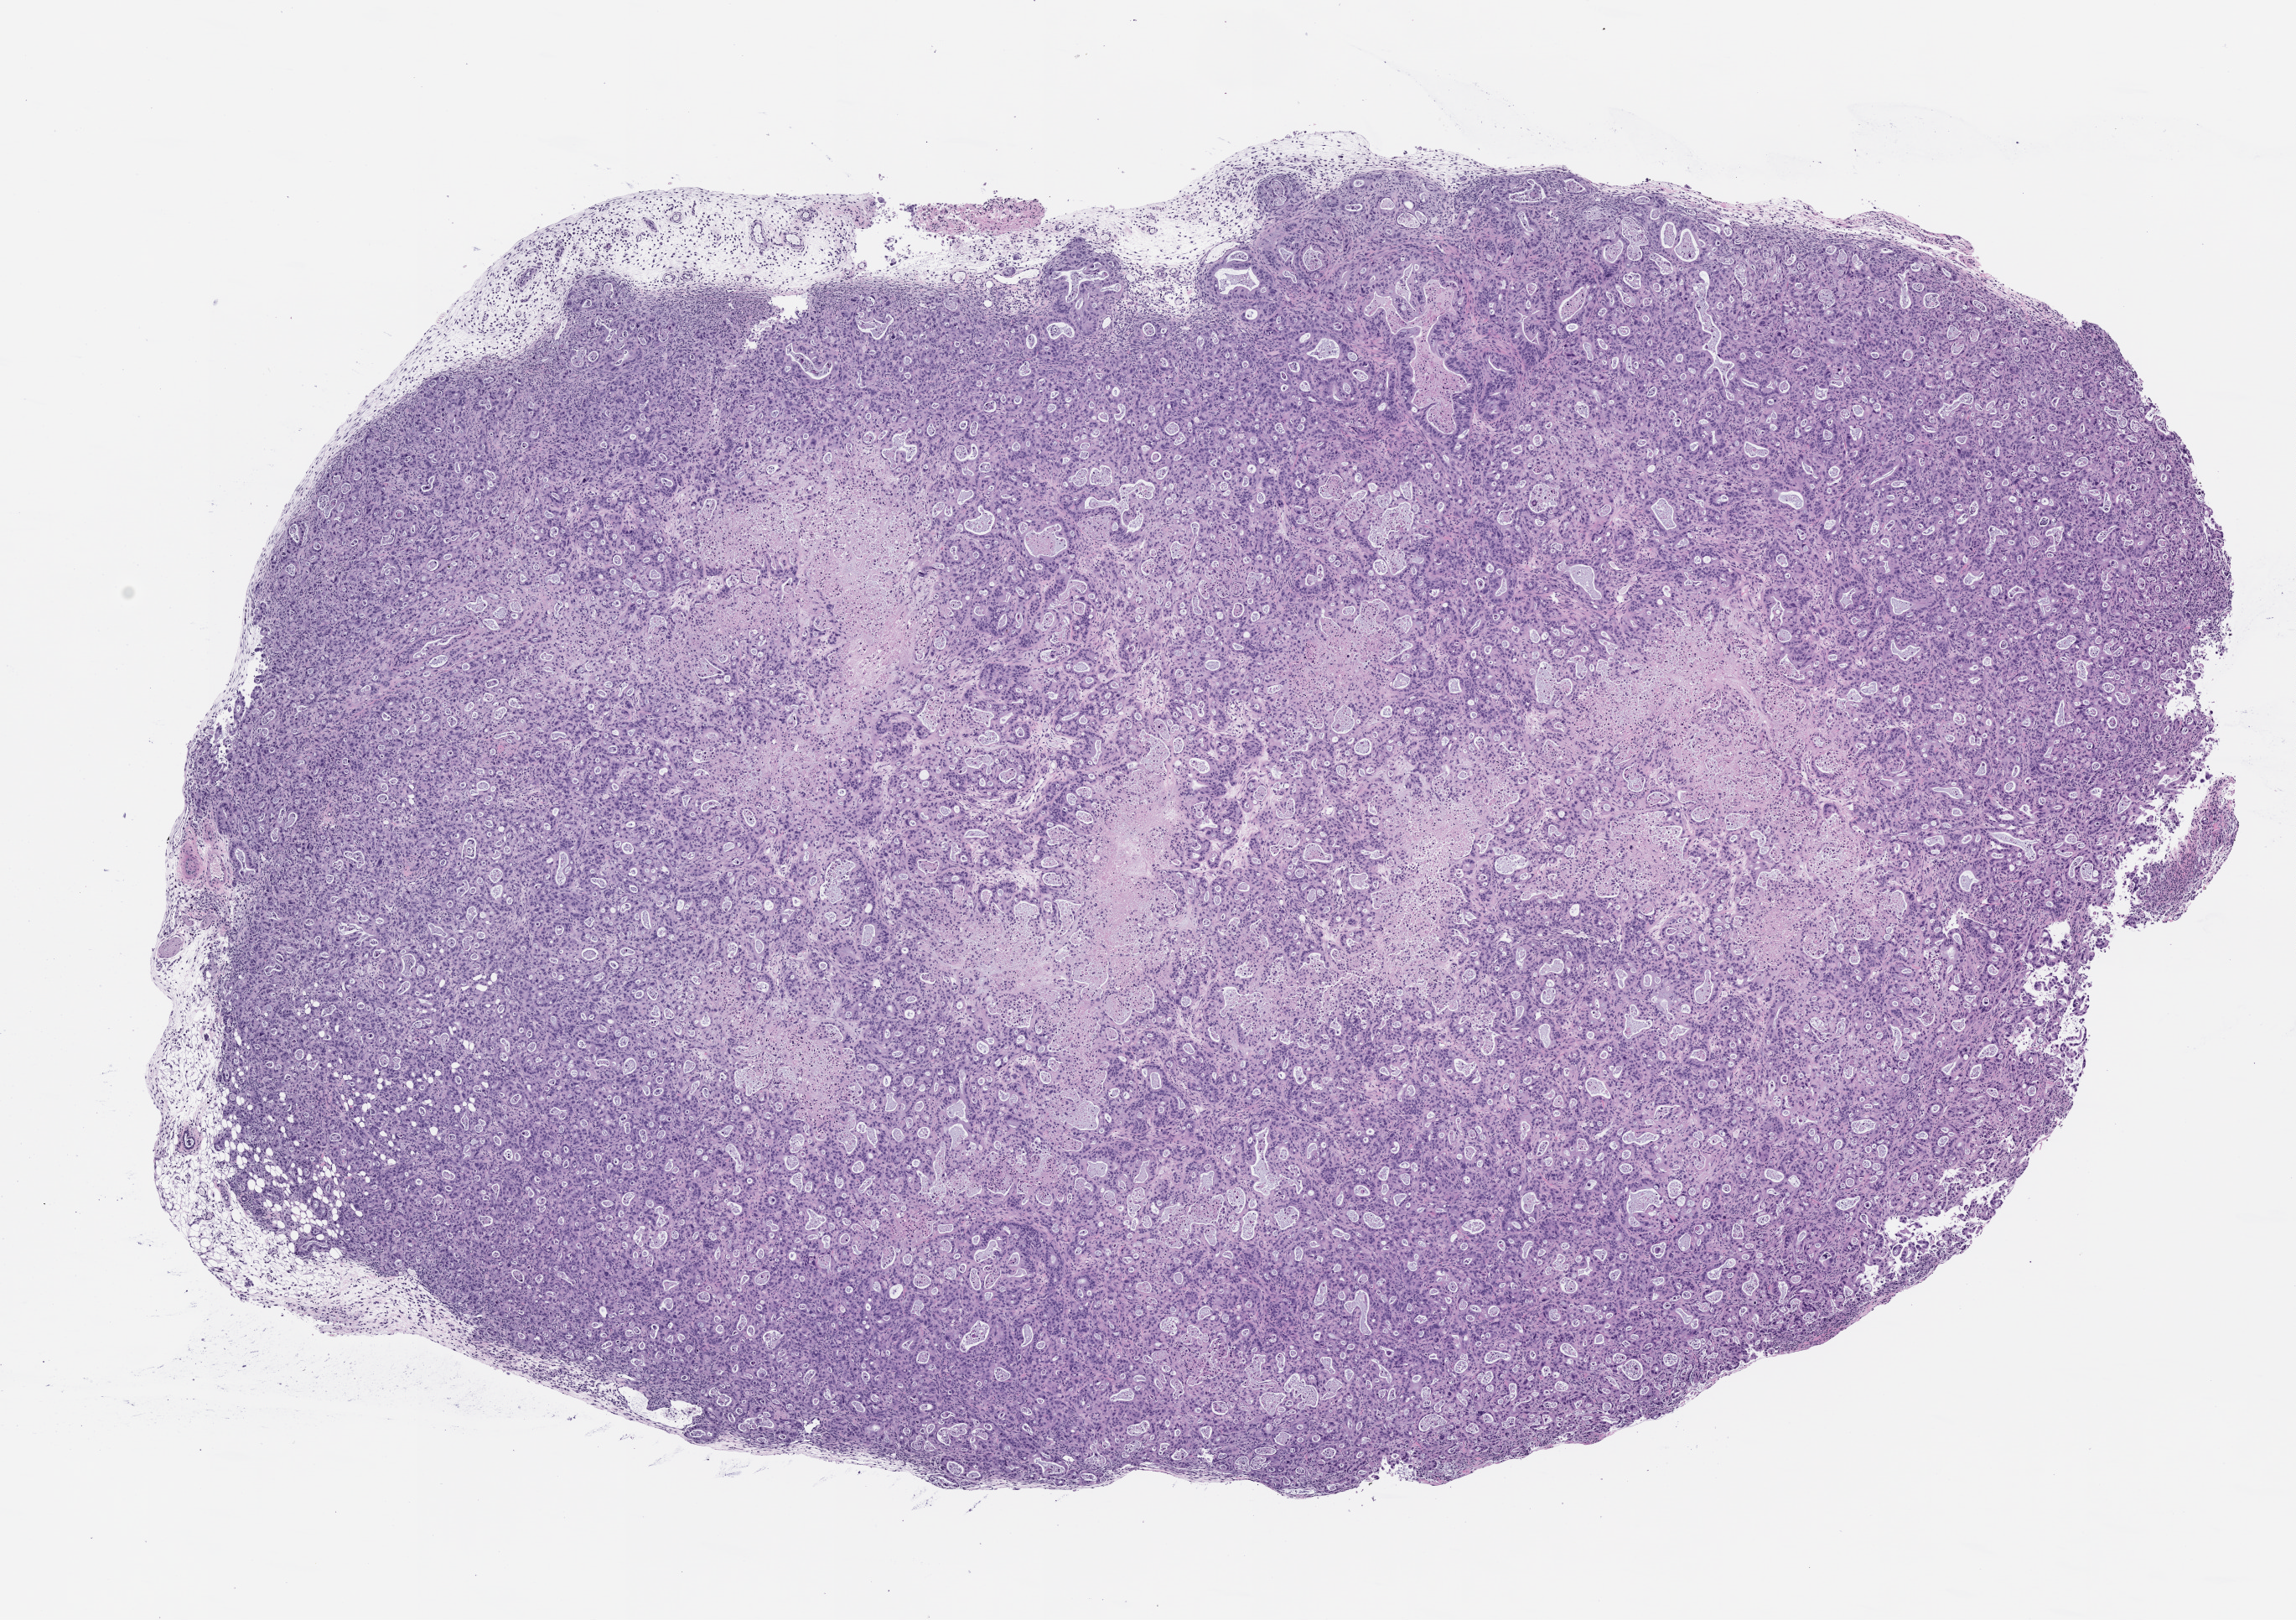
Whole-slide image, haematoxylin and eosin: patient-derived xenograft (human tumor grown in a mouse), passage 1 — low-resolution overview of the scanned area, about 11.0 x 7.8 mm. Formalin-fixed paraffin-embedded section. Tumor site category: pancreas.
Originating patient diagnosis: Pancreatic Adenocarcinoma.